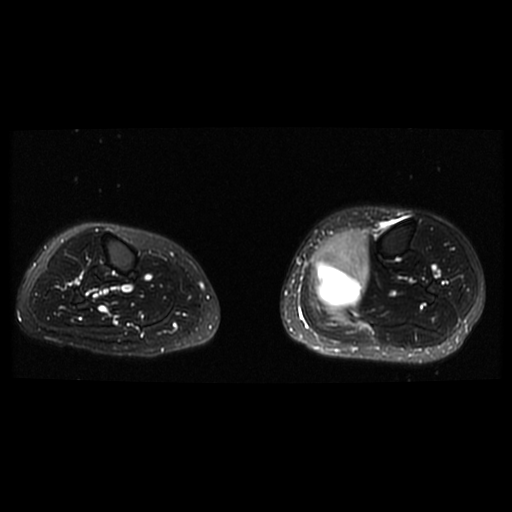
MRI of an extremity soft-tissue mass, one axial slice; position 12 of 38 along the scan axis; T2-weighted fat-saturated; 6 mm slice thickness; 512 × 512 image matrix, field of view 330 × 330 mm. Female patient. Case-level facts recorded for this patient, not image findings: histological type: extraskeletal high grade osteogenic sarcoma; grade: high; site of the primary tumour: left calf.
Outlined on this slice (expert manual segmentation):
- gross tumour volume (mass): bounding box [x1, y1, x2, y2] px = [313, 230, 371, 309]